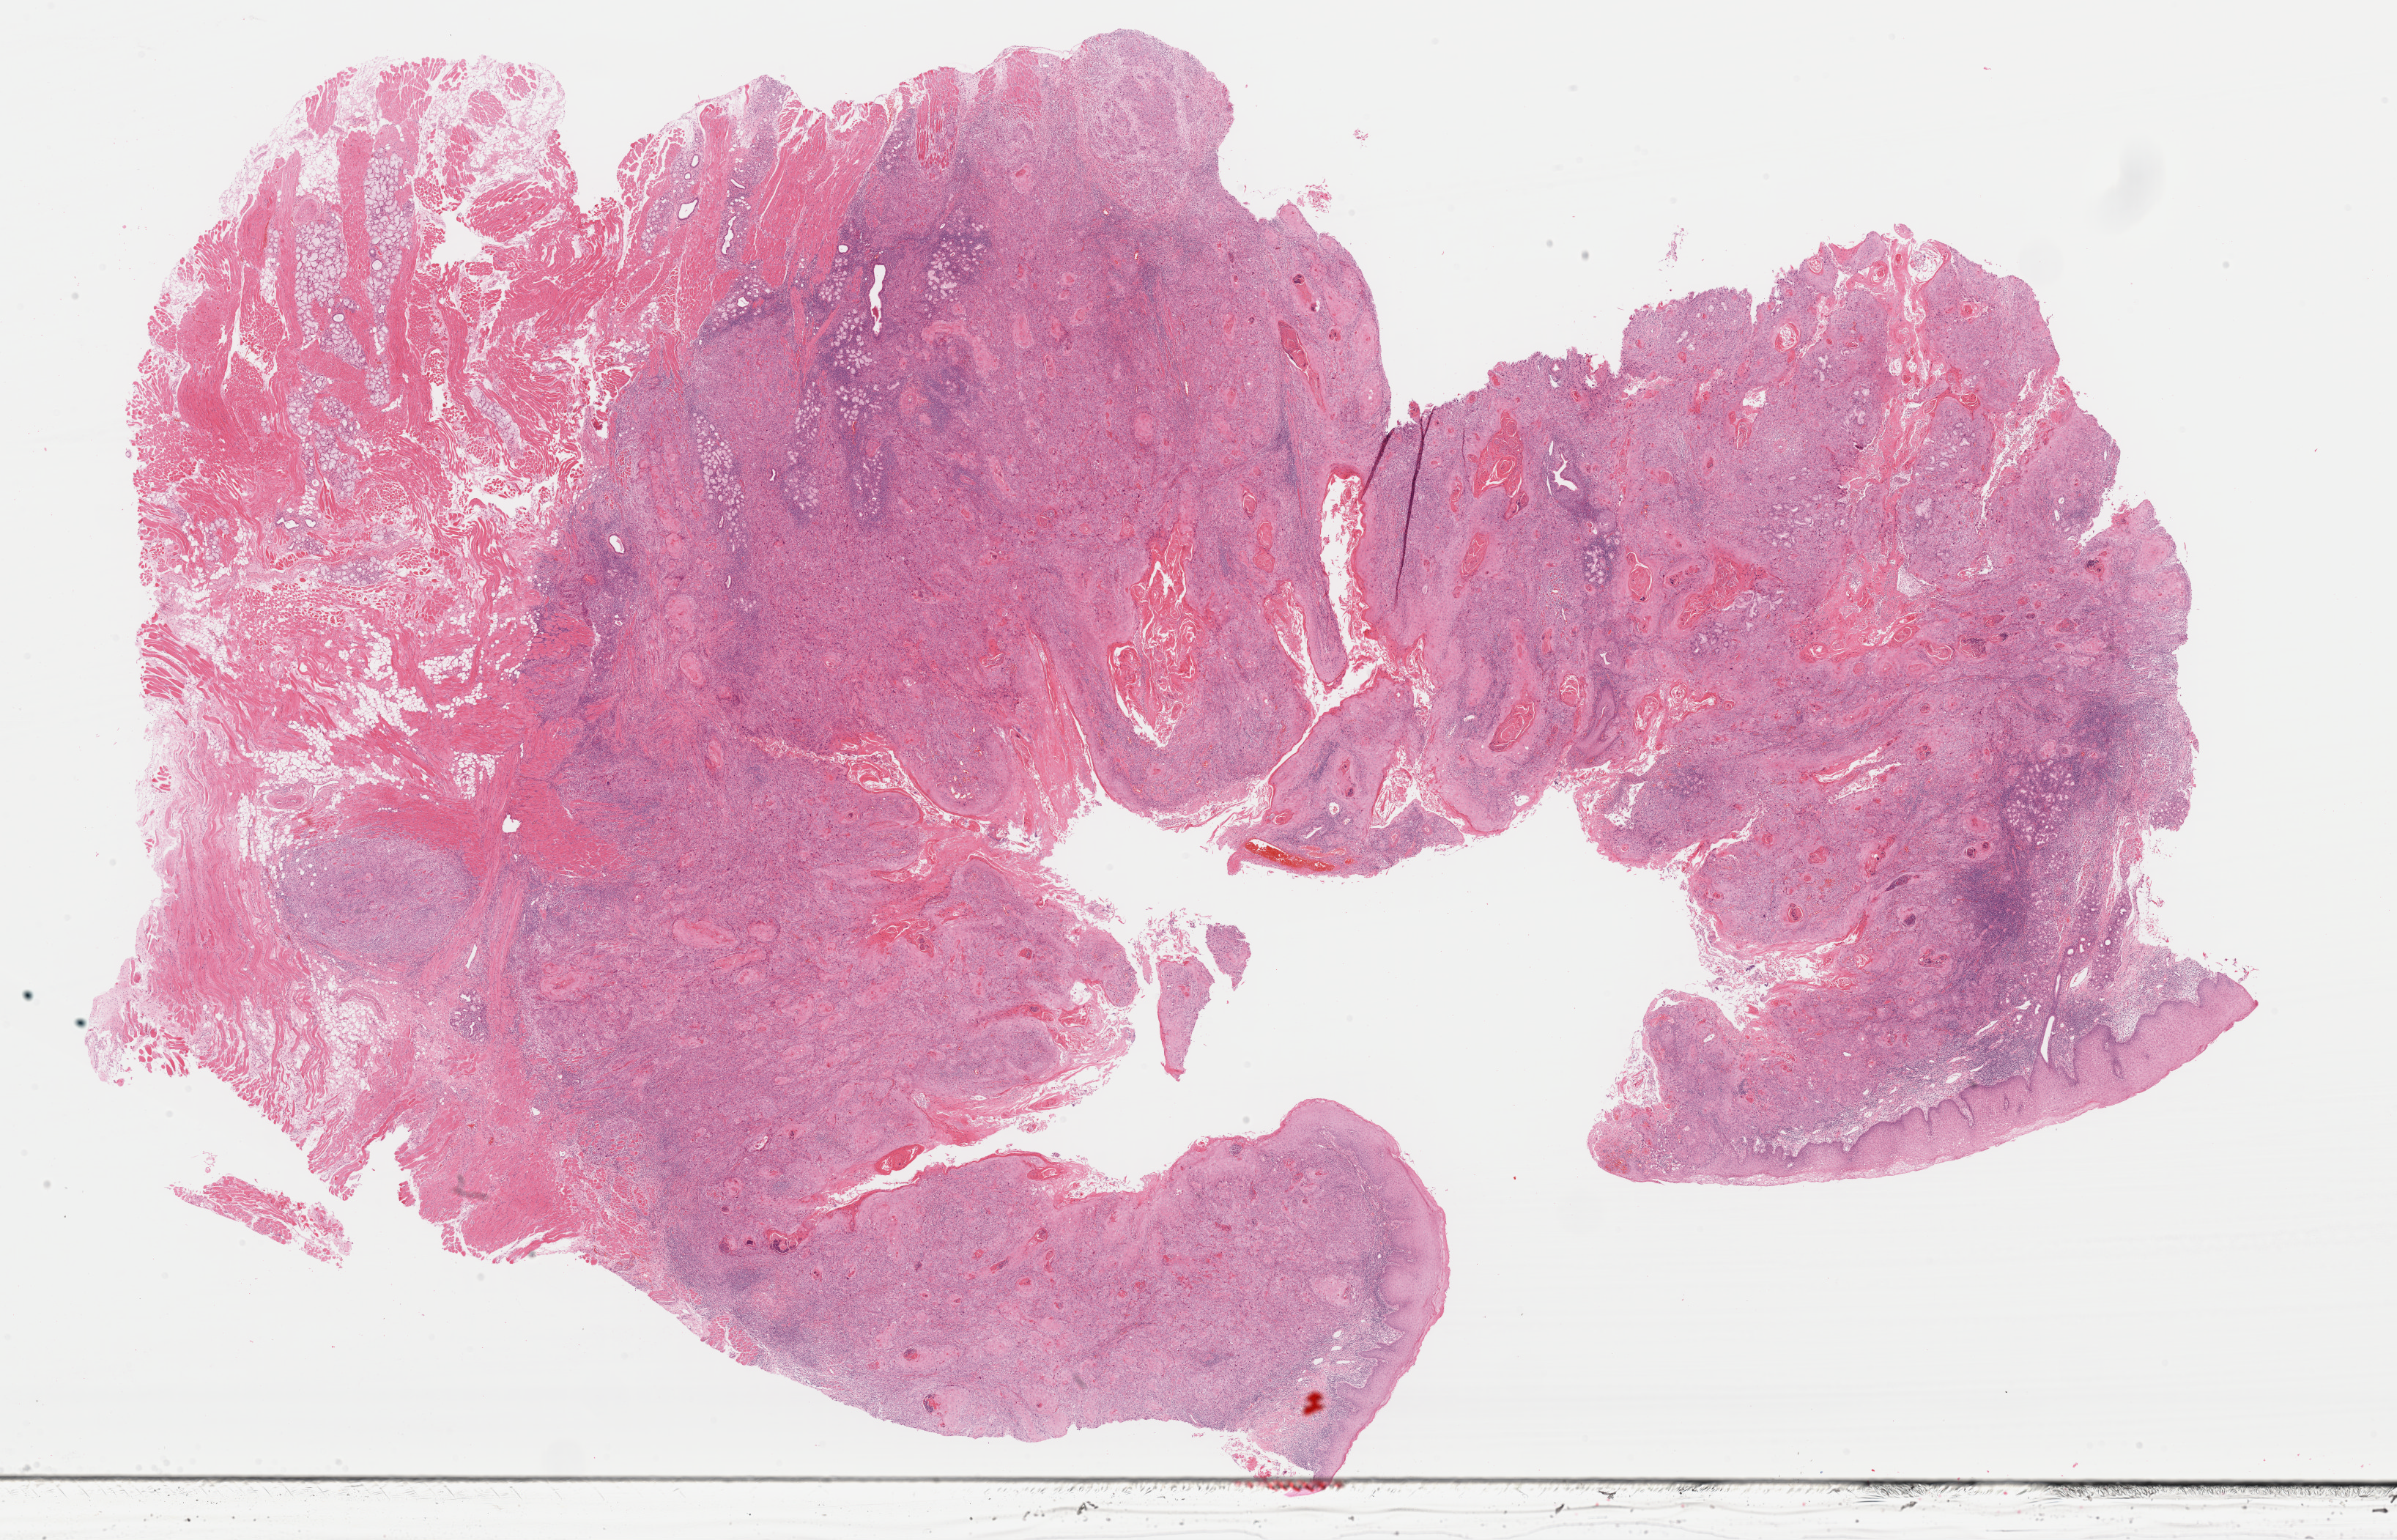
H&E-stained whole-slide image, a low-resolution overview of the entire scanned area, about 25.8 x 16.6 mm; FFPE section; sample: primary tumour, head and neck. Male, age 62 years at initial diagnosis. Histologic grade: G1 (well differentiated).
- AJCC pathologic stage: III (7th edition)
- pathologic diagnosis: Squamous cell carcinoma, keratinizing, NOS (tongue, NOS)
- TNM: T3 N0 M0